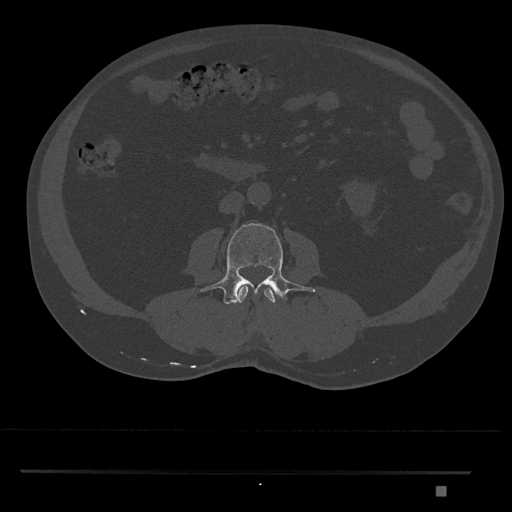
CT including the spine, one axial slice; position 696 of 1134 along the scan axis; 120 kVp; bone window (W 1800 / L 400 HU); 0.5 mm slice thickness; 512 × 512 image matrix, field of view 429 × 429 mm. Male patient, age 65 years. From the clinical record (not read from this slice): primary cancer: prostate.
Outlined on this slice (semi-automatic segmentation, software-assisted and operator-edited):
- L2 vertebra: bounding box (x1, y1, x2, y2) in pixels: (237, 285, 276, 303)
- L3 vertebra: (200, 223, 315, 304)